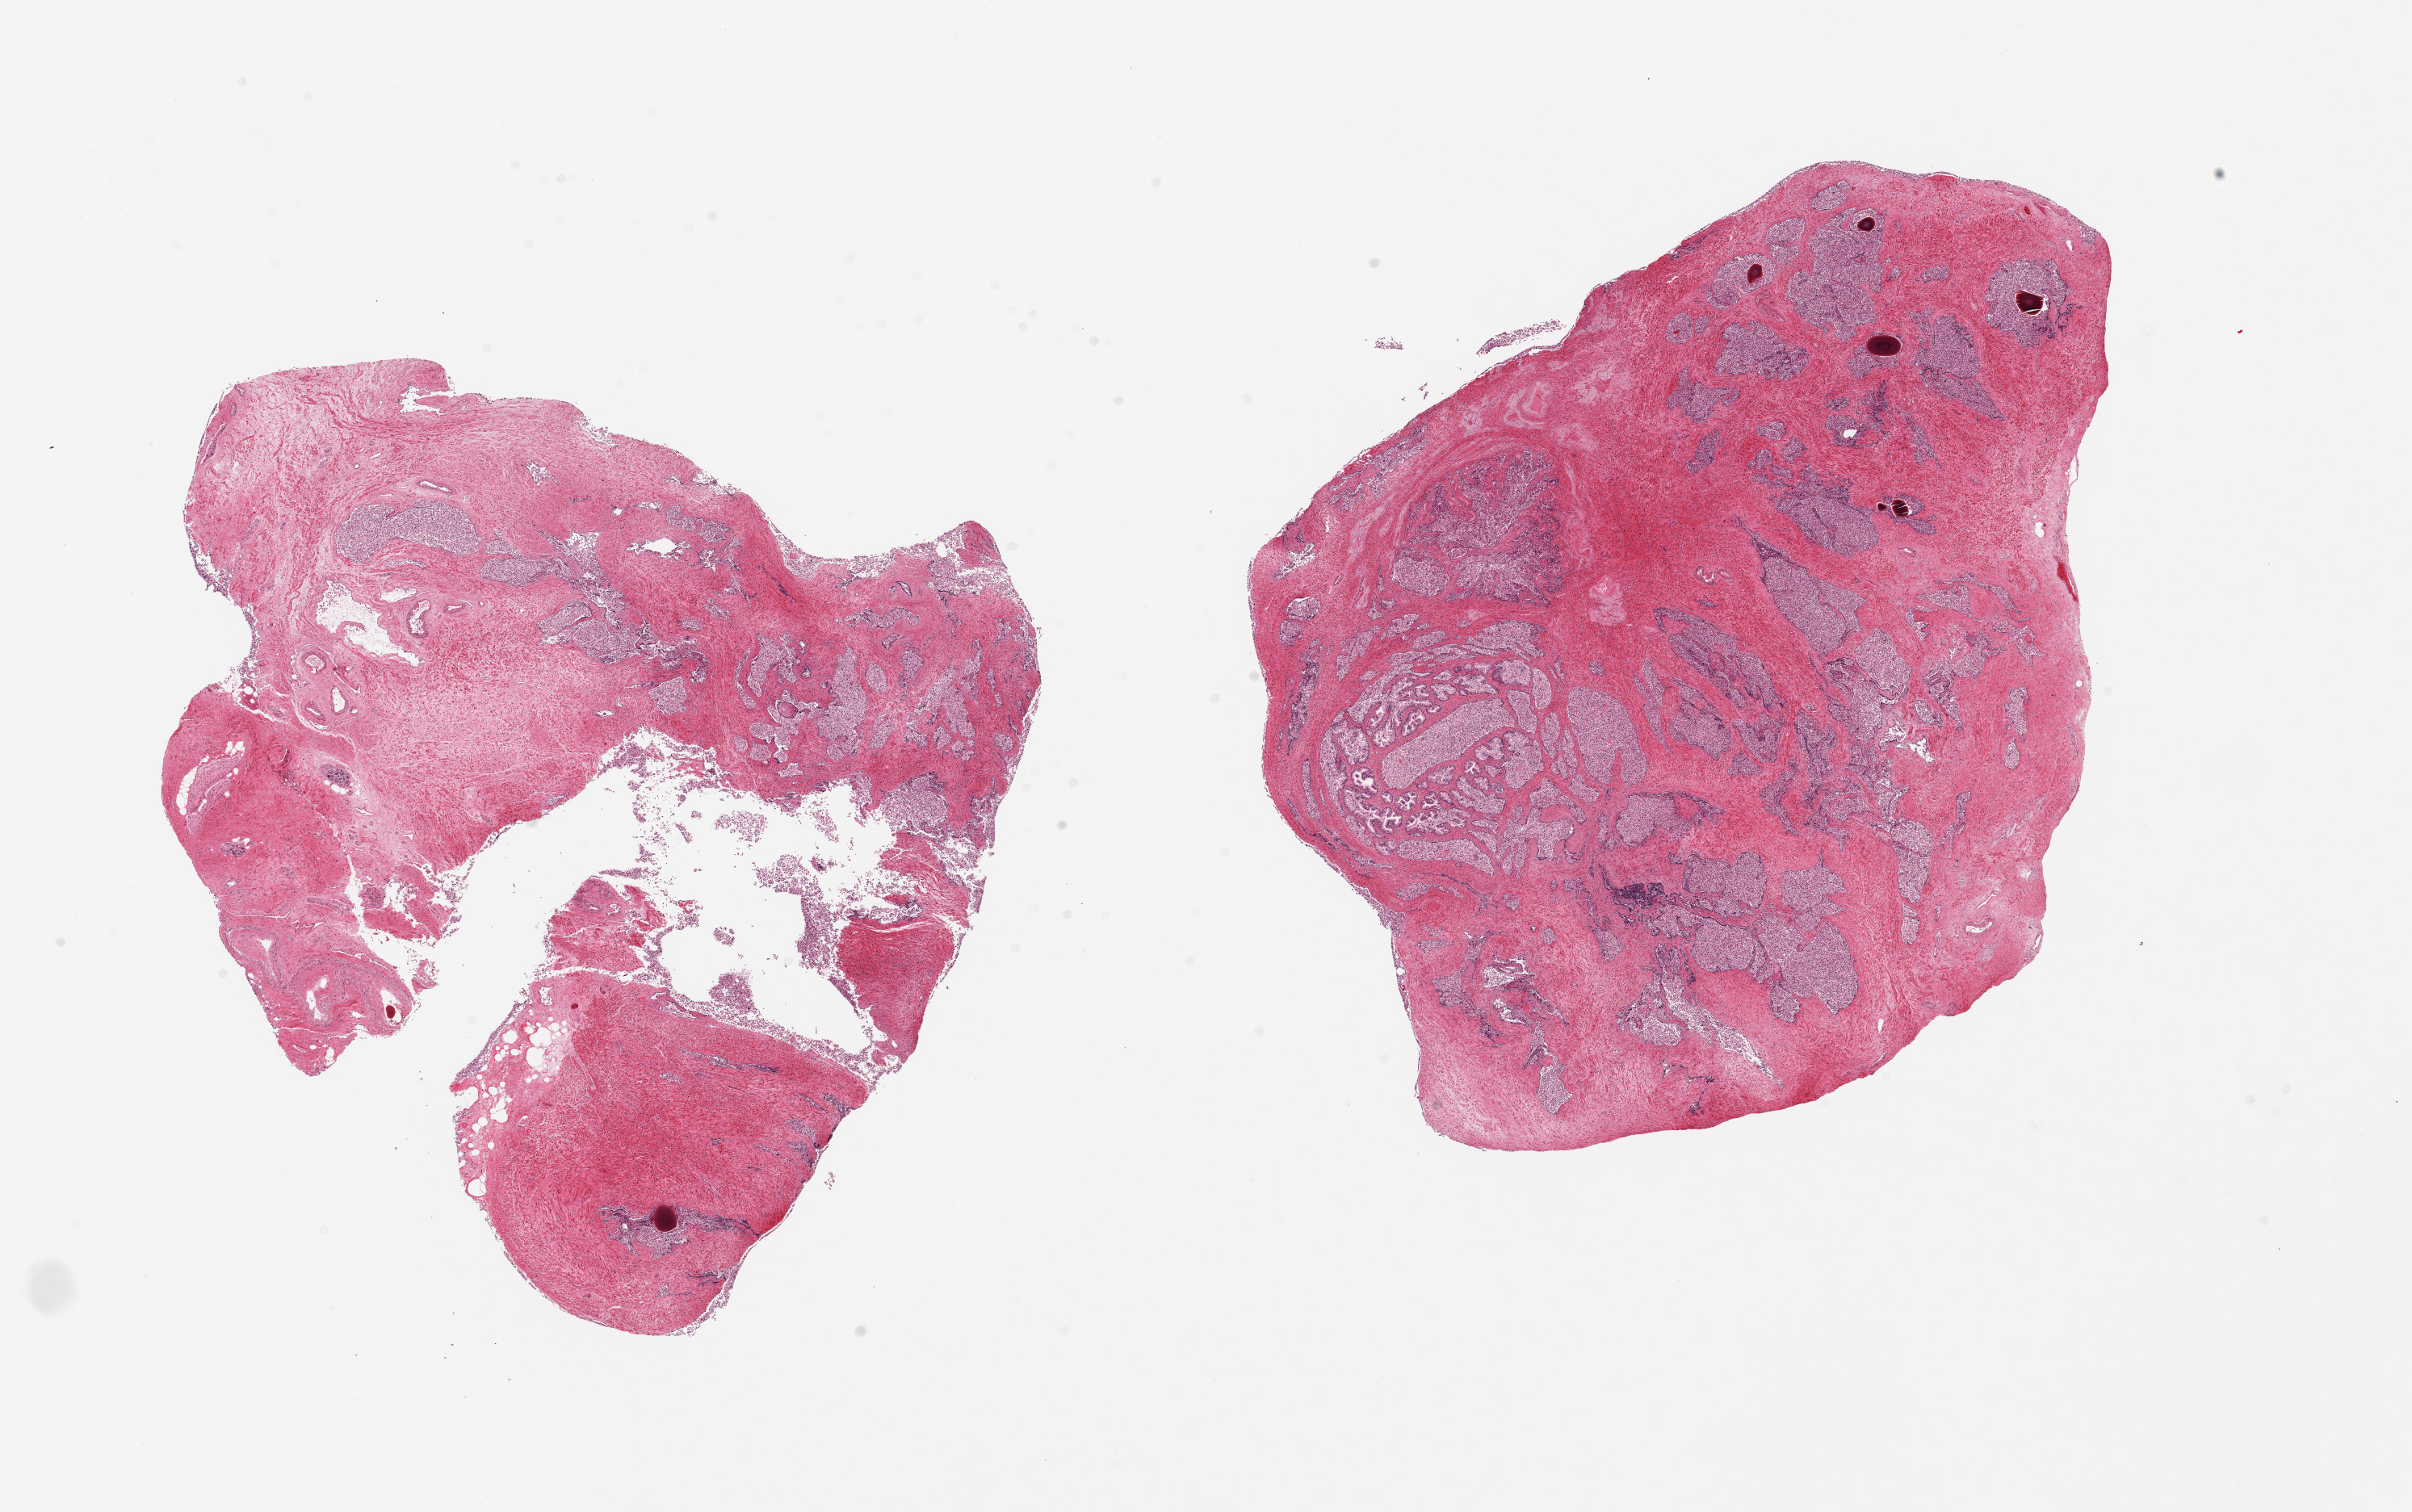
Whole-slide image, haematoxylin and eosin stain — low-resolution overview of the scanned area, about 23.6 x 14.8 mm, PAXgene-fixed paraffin-embedded (PFPE) section, target tissue: prostate, tissue donor sample. Donor: male.
• reviewer comment on this tissue sample: 2 pieces; fibromuscular stroma and glands with massive sloughing of glandular epithelium, scattered corpora amylacea